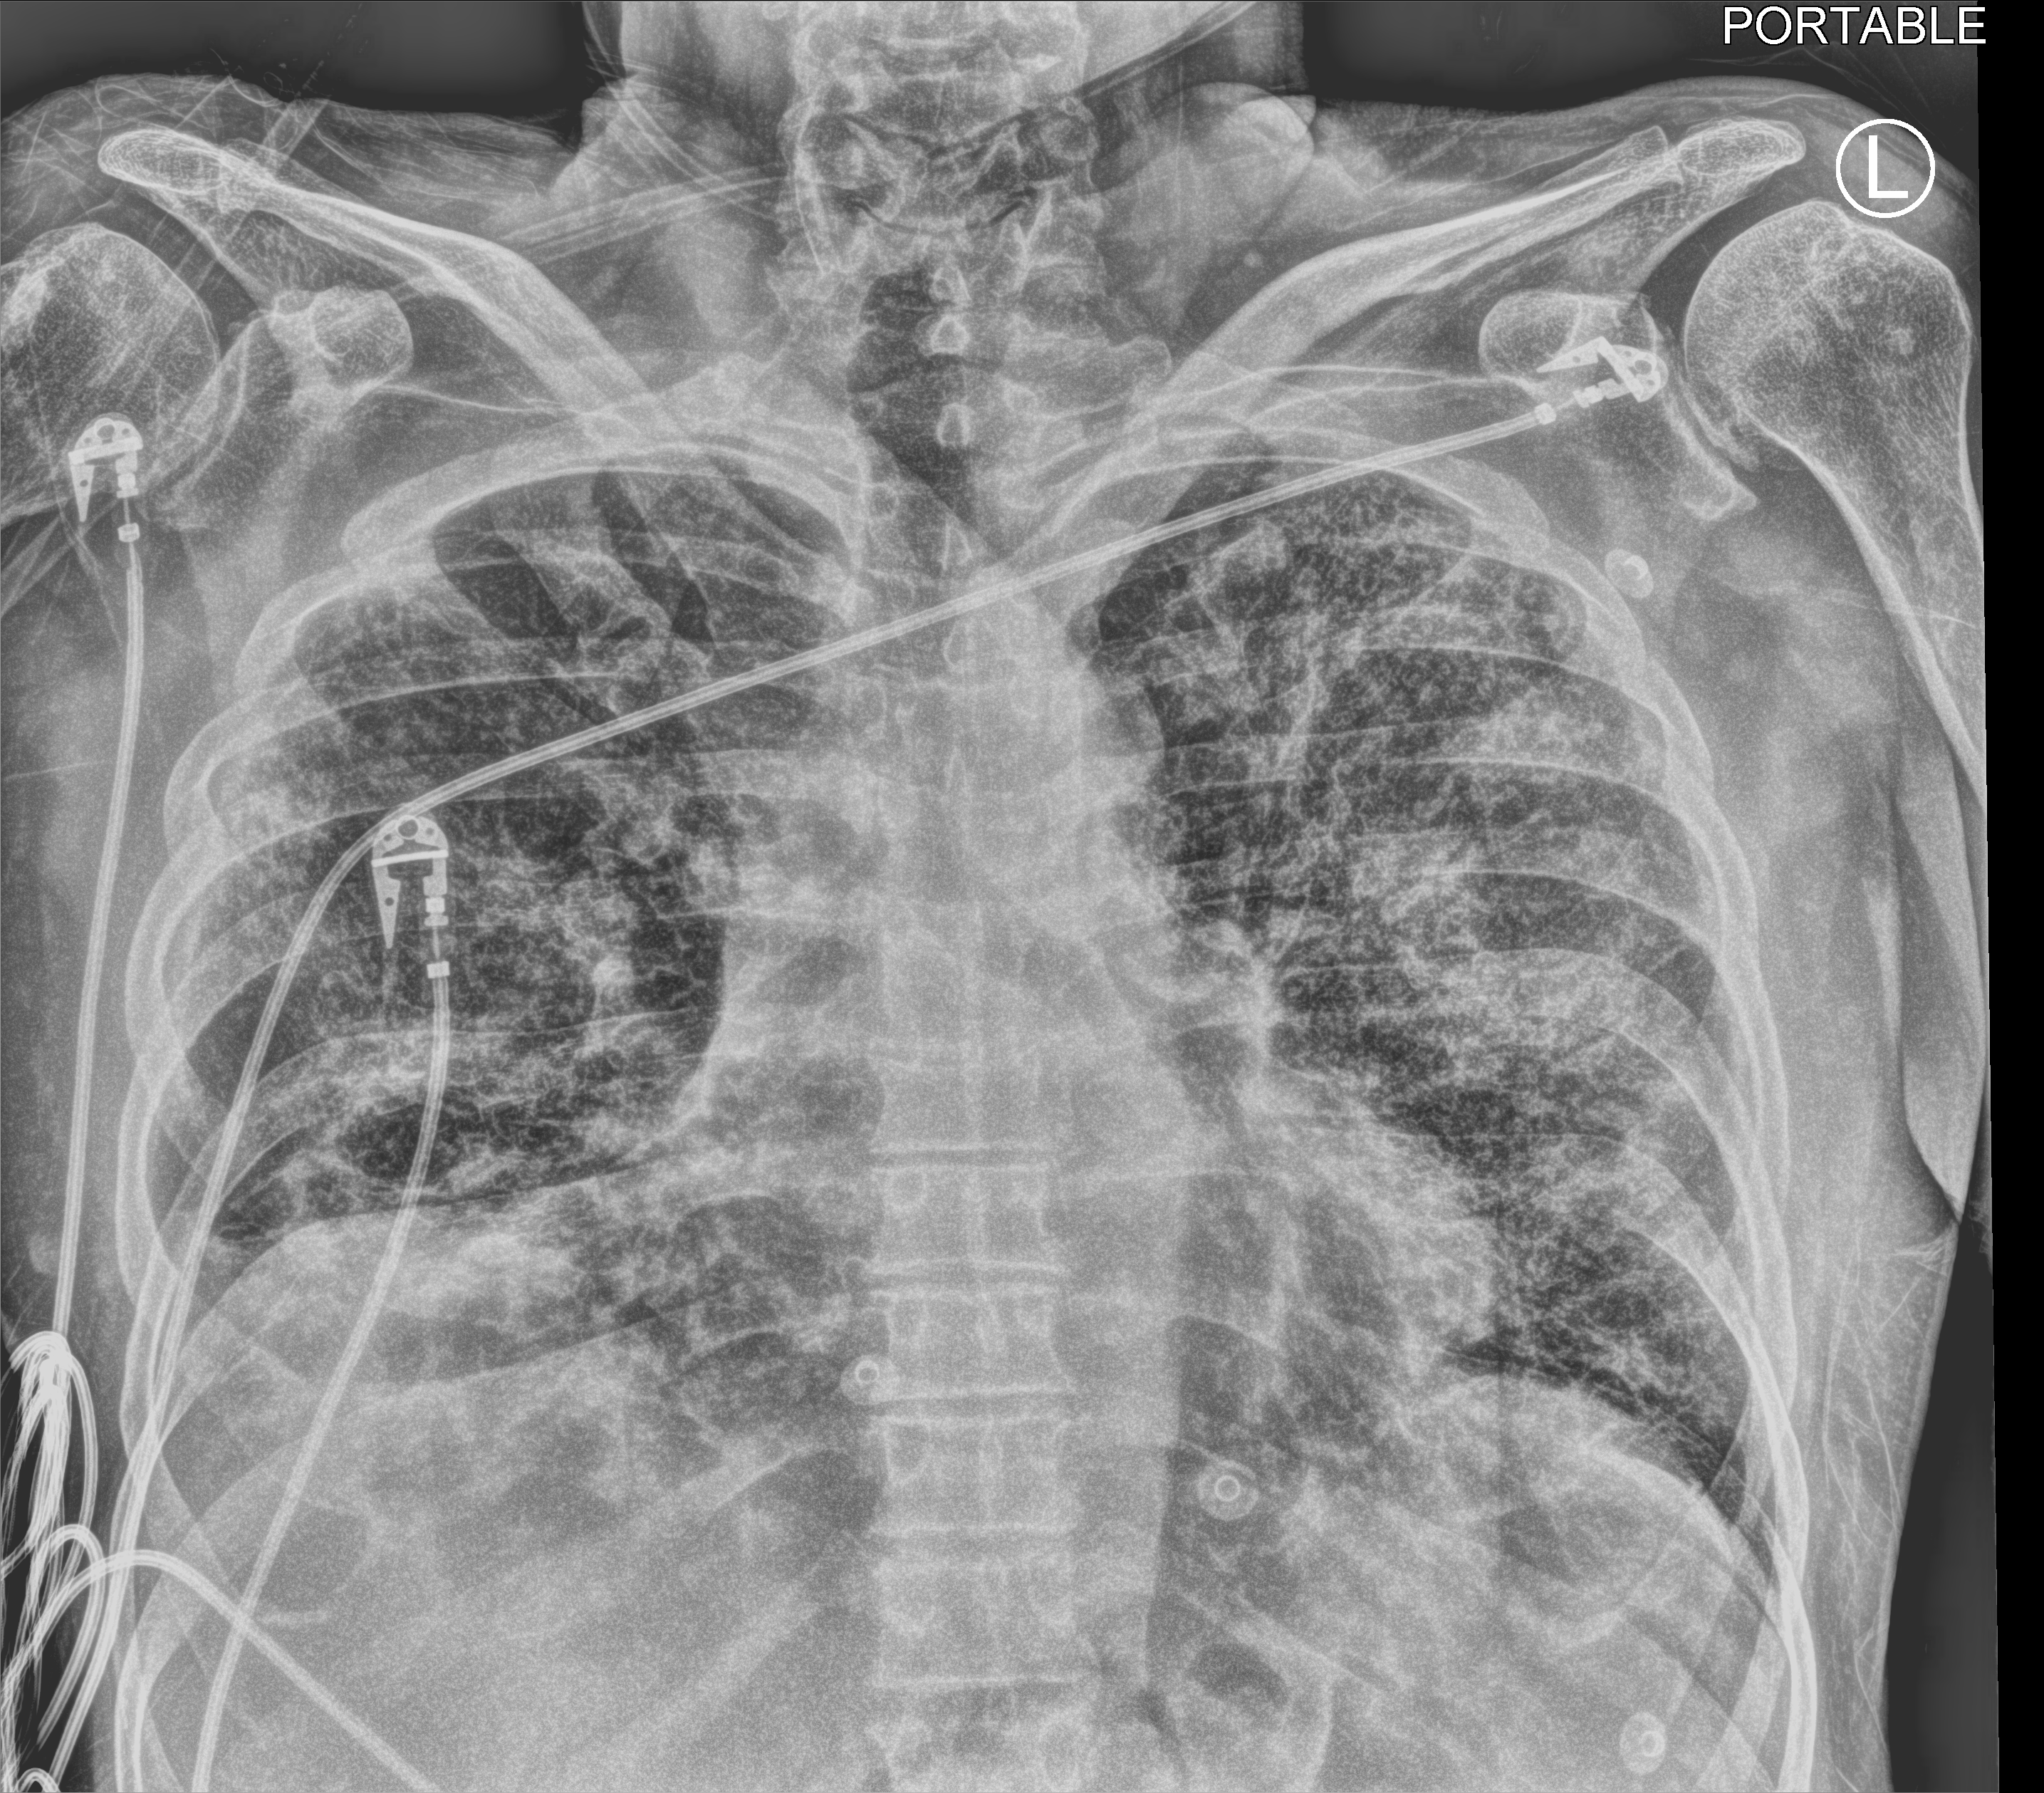
Bedside chest radiograph (computed radiography); anteroposterior (AP) projection. Patient hospitalised with COVID-19; male, aged 60–74 years.
Hospital-stay facts (about this admission, not read from this image; timing relative to this image not recorded): admitted to intensive care during this hospital stay: no; mechanically ventilated during this hospital stay: no.